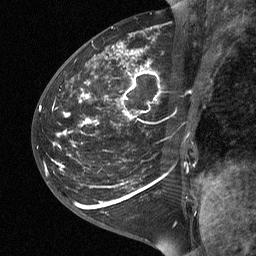
Breast MRI (dynamic contrast-enhanced), one sagittal slice. Dynamic contrast-enhanced study with each time point stored as its own series, time point 2 of 3 at this slice position (early post-contrast, ordered by acquisition time). 1.5 T. TE 4.8 ms, TR 27 ms. 2 mm slice thickness. 256 × 256 image matrix, field of view 200 × 200 mm. Patient: female, 42 years. From the clinical record (not read from this slice): setting: breast cancer imaged before/during neoadjuvant chemotherapy; receptor status: triple-negative.
Structures marked on this image (semi-automatic segmentation, software-assisted and operator-edited):
- analysis volume of interest (the breast-tissue region the enhancement analysis was run in; not a lesion): bounding box <43,29,203,190> (left, top, right, bottom; pixels)
- tumour enhancement mask (voxels above the 90 % enhancement threshold inside the analysis volume of interest): <87,46,156,122>